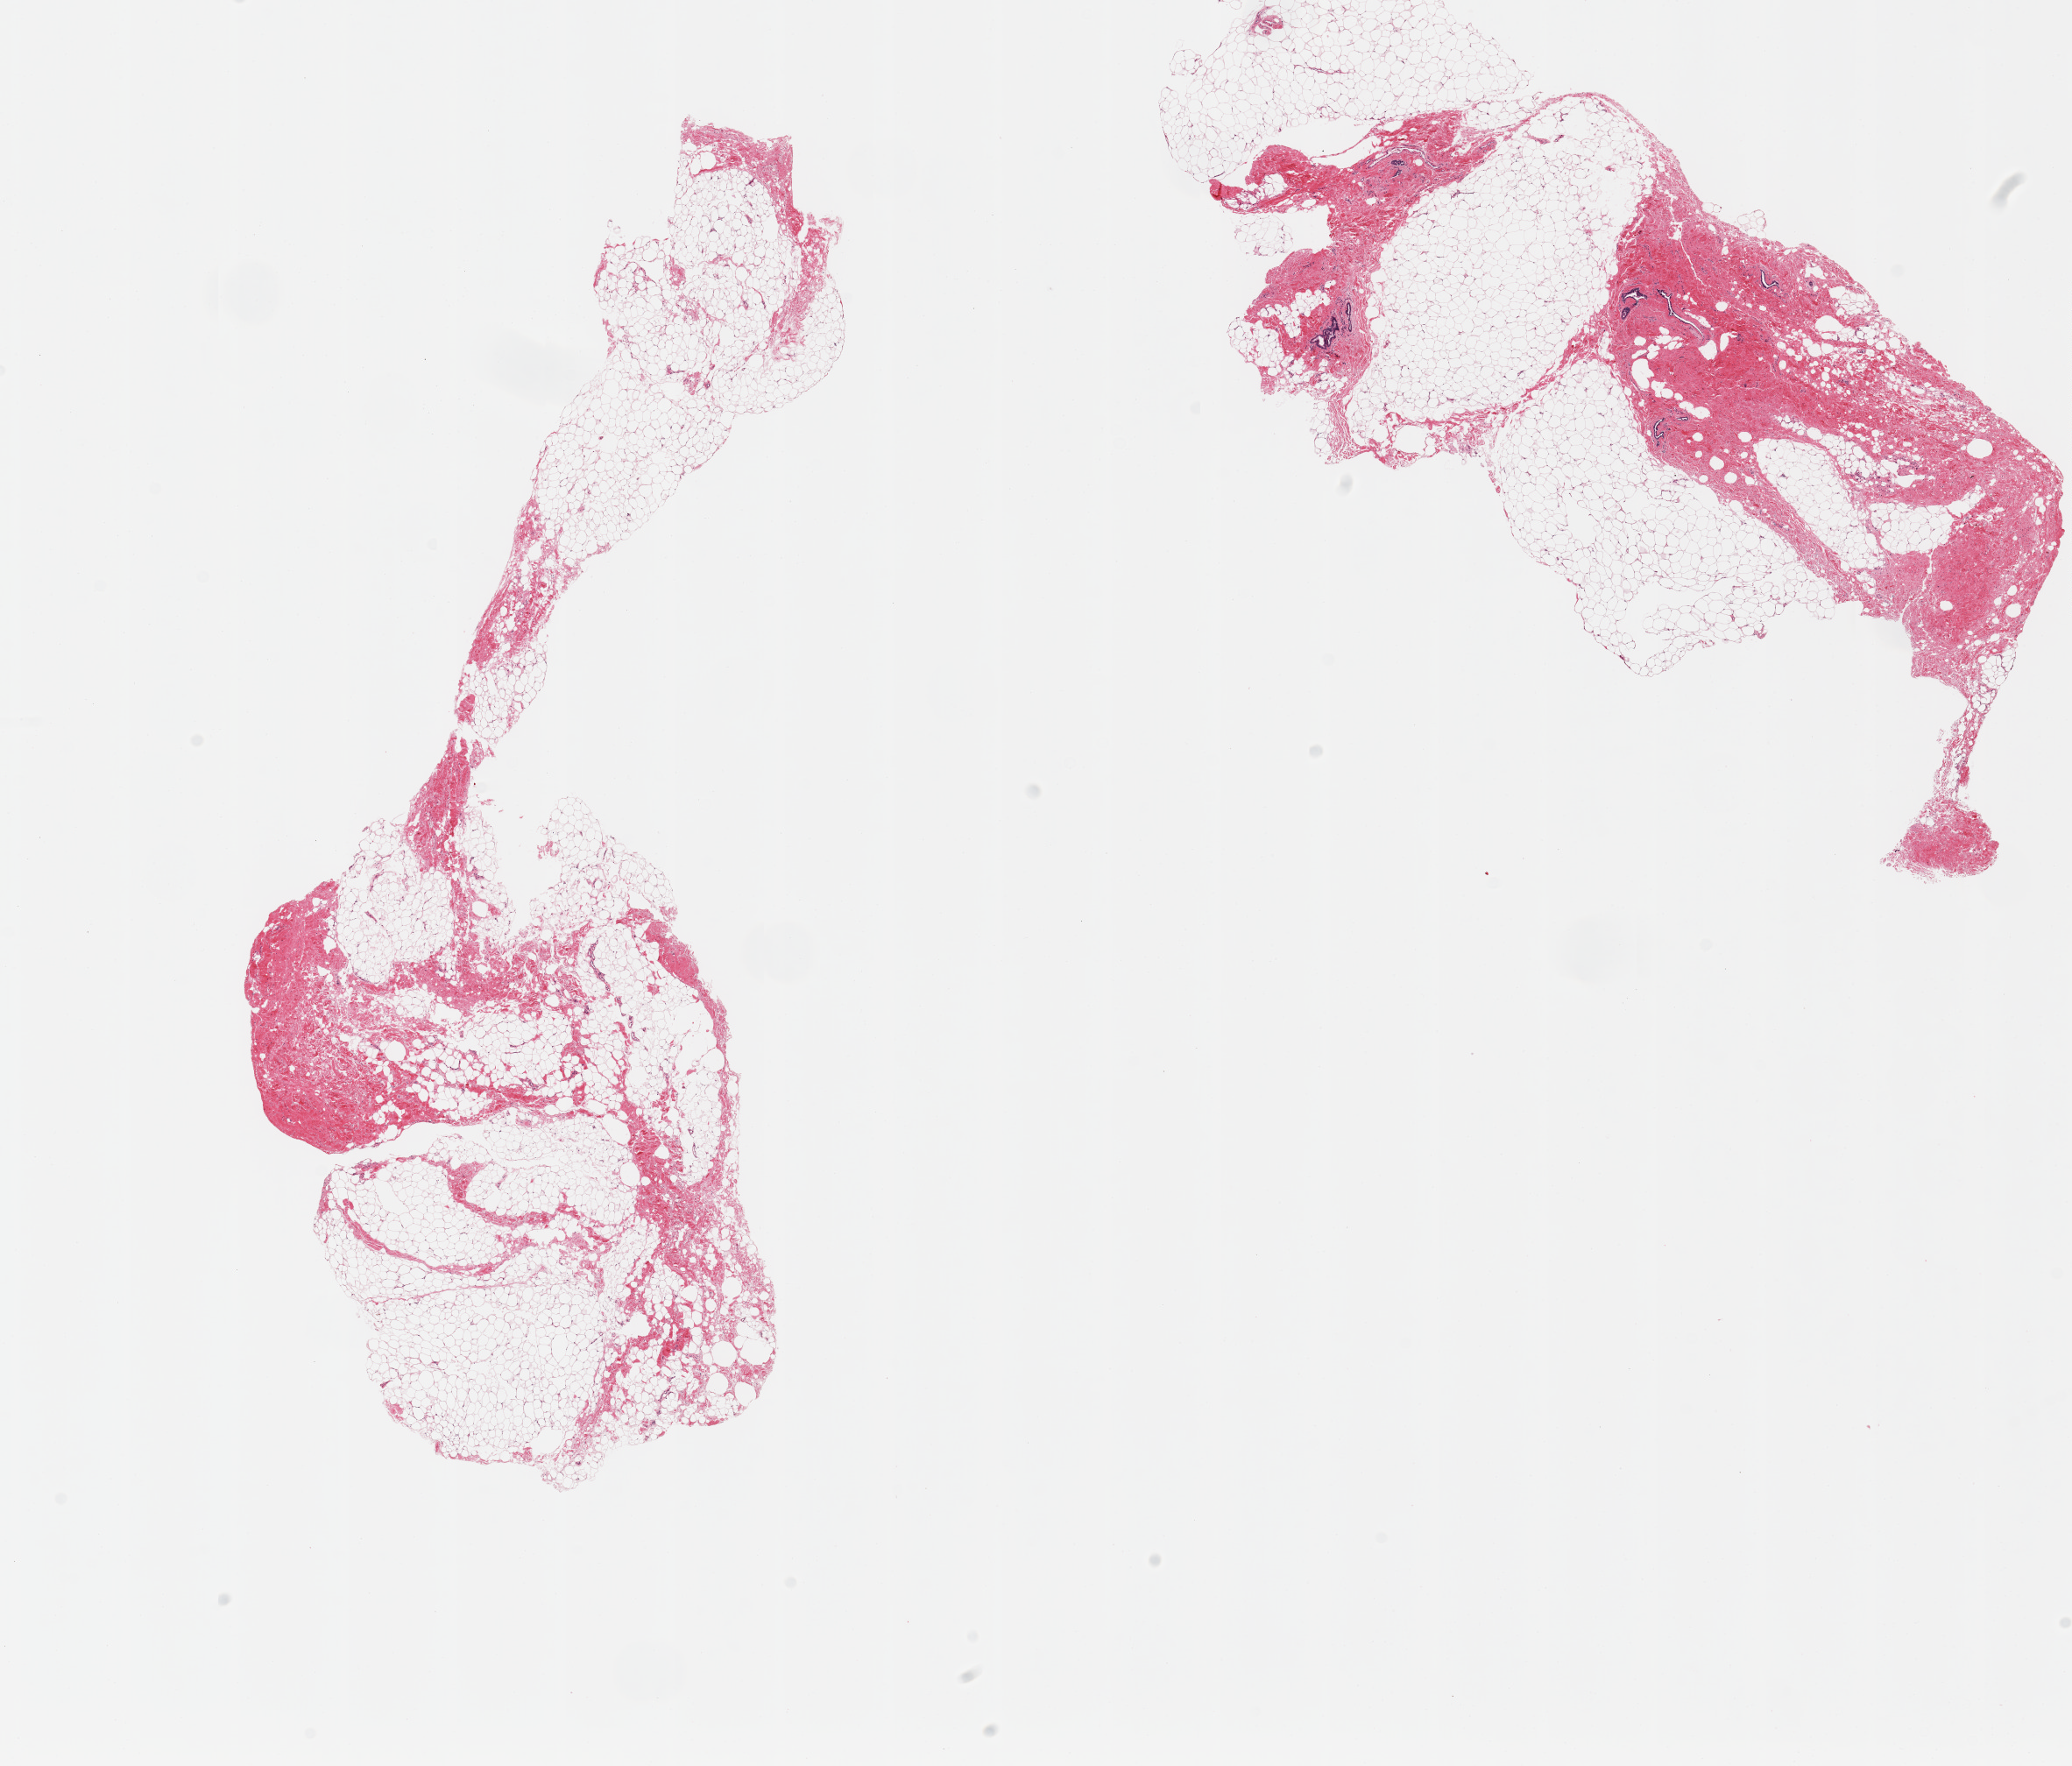
Haematoxylin and eosin whole-slide image, brightfield — shown as a low-resolution overview of the whole scanned area (about 18.7 x 15.9 mm, from a 20x scan); PAXgene-fixed, paraffin-embedded tissue; section of breast (target tissue); donor tissue sample. Donor sex: male.
* pathologist's review note for this sample: 2 pieces, fibroadipose tissue, no ductal elements